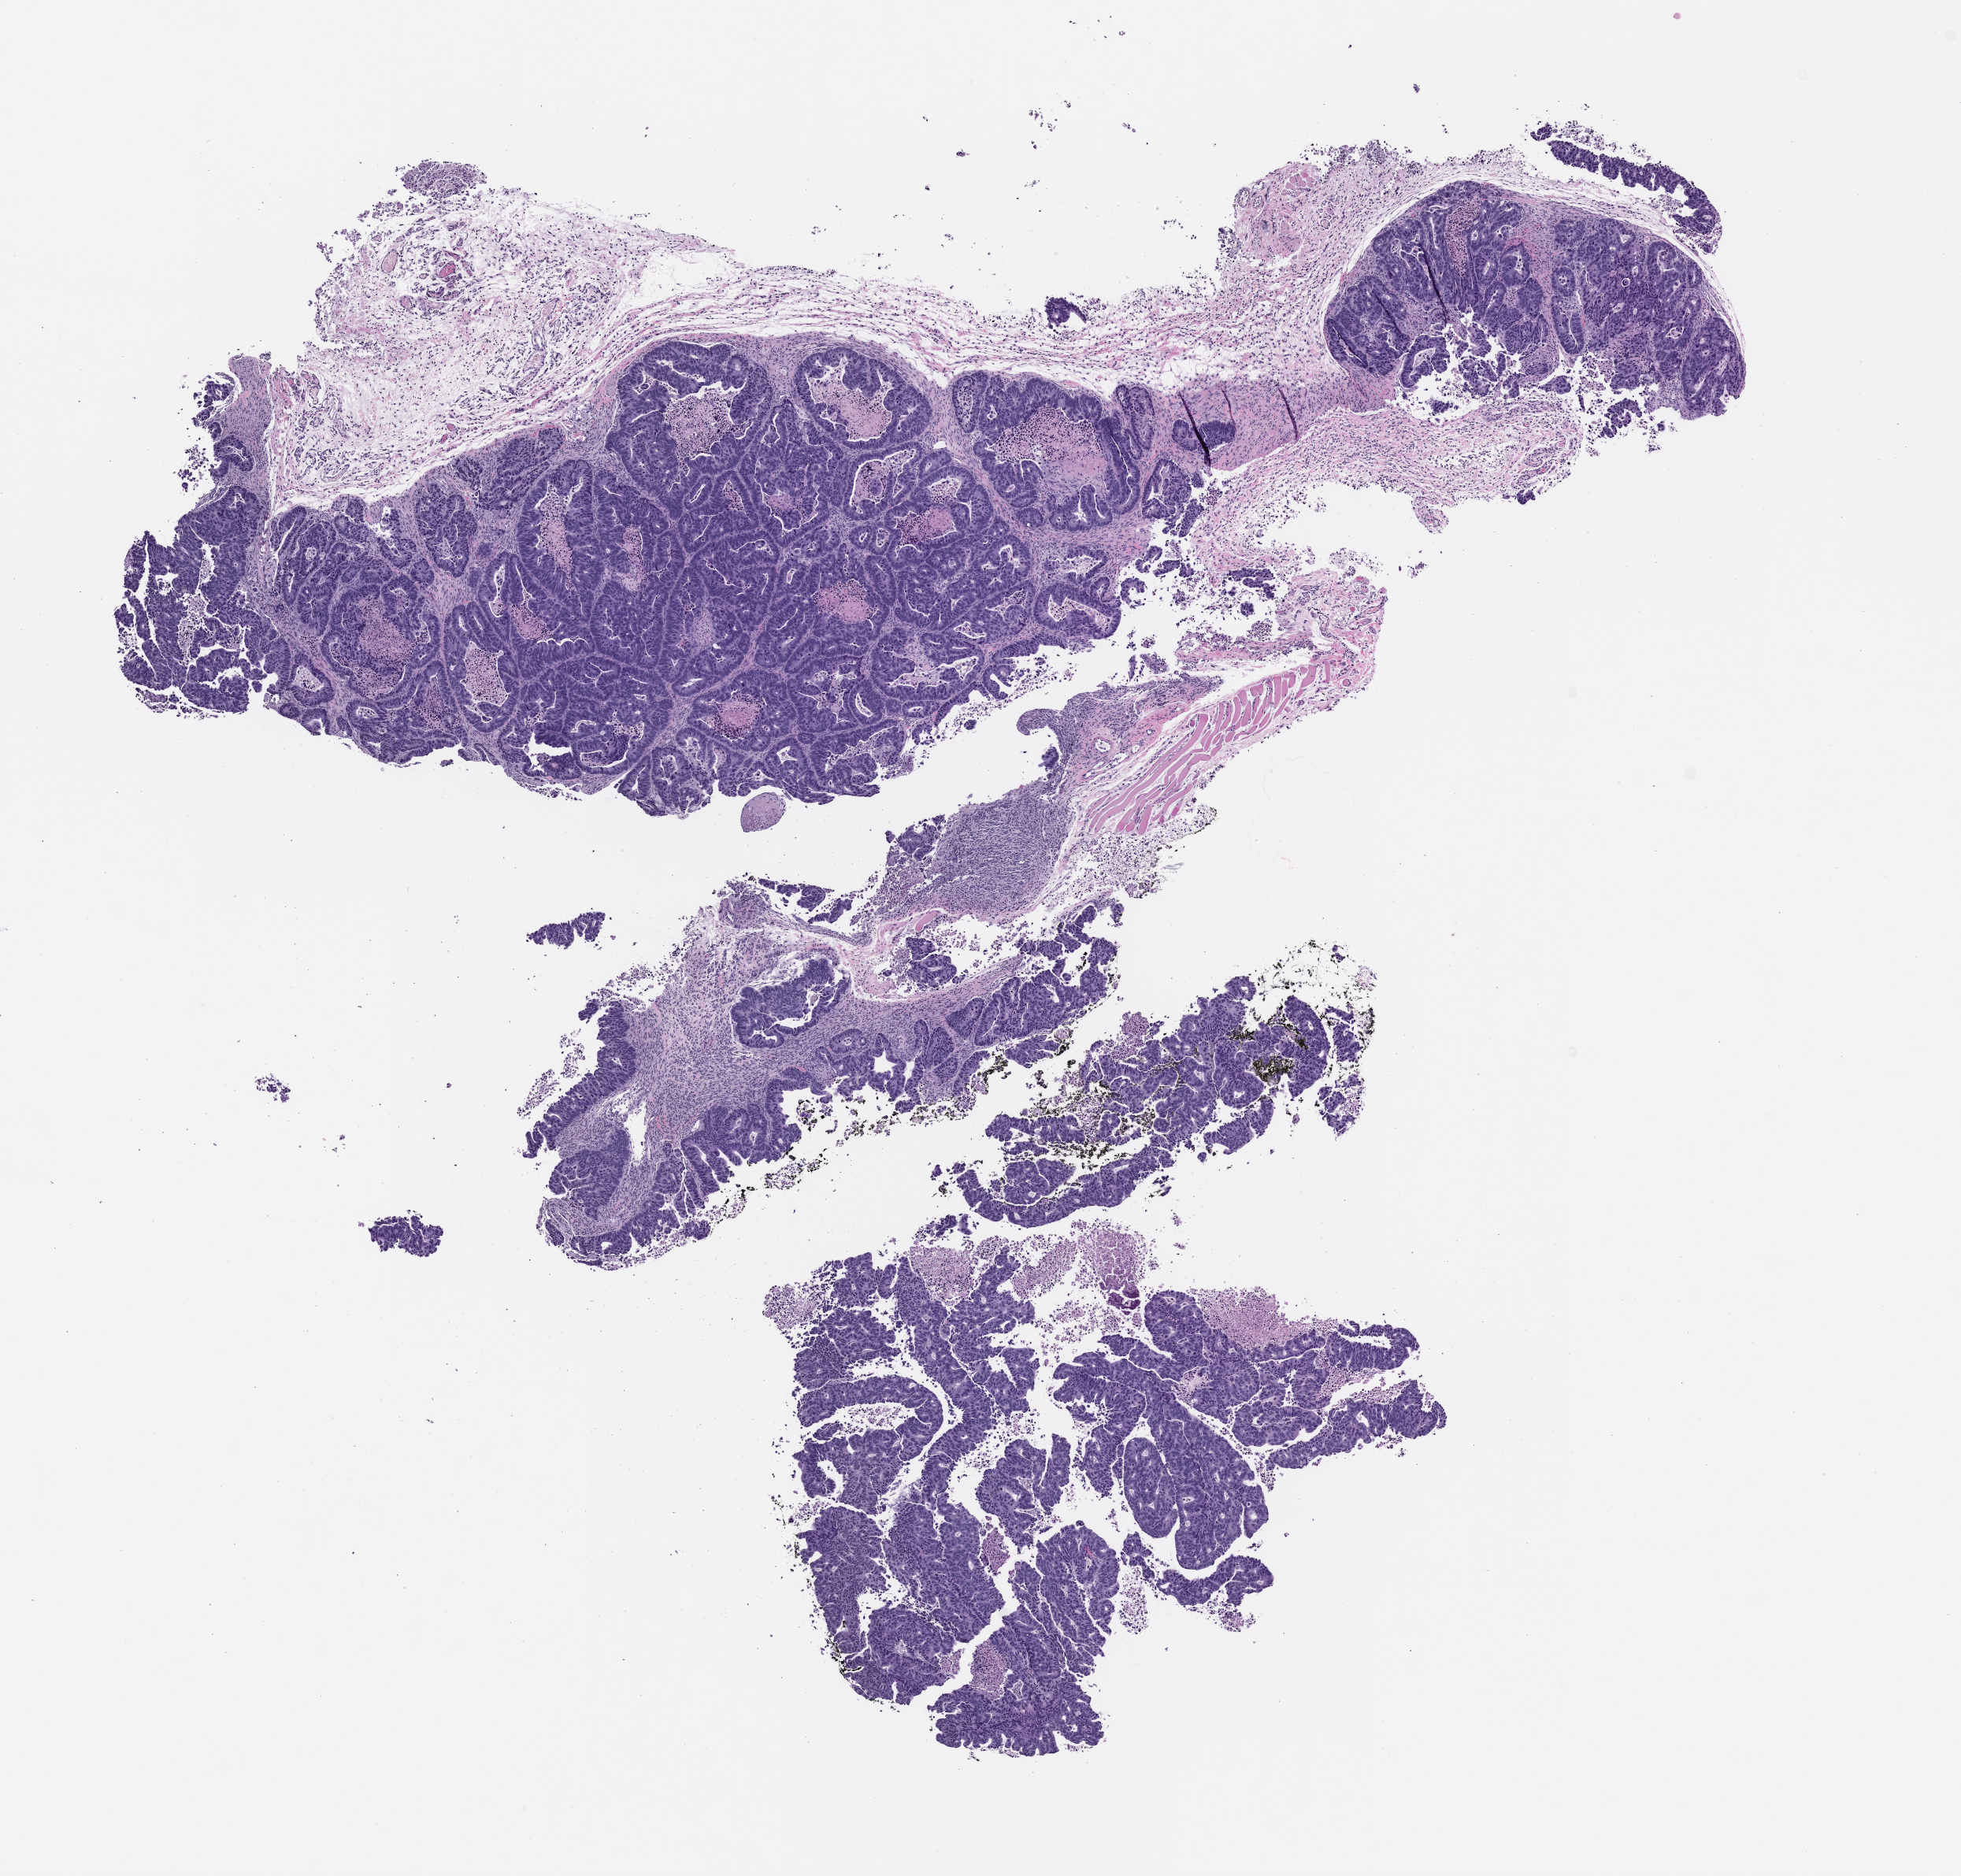
Haematoxylin and eosin whole-slide image of a patient-derived xenograft (PDX) tumor grown in a mouse, passage 0 — a low-resolution overview of the entire scanned area, about 10.0 x 9.6 mm, FFPE section, tumor site category: rectum.
Originating patient diagnosis: Rectal Adenocarcinoma.